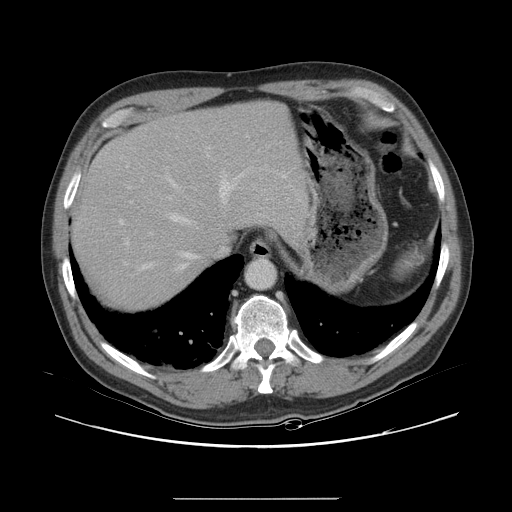
Contrast-enhanced abdominal CT, one axial slice; slice 25 of 40 in the series (ordered by position); 120 kVp; soft-tissue window (W 400 / L 40 HU); 5 mm slice thickness; 512 × 512 image matrix. Male patient, age 64 years. Case-level facts recorded for this patient, not image findings: diagnosis: colorectal cancer liver metastases, imaged before liver resection; multiple liver metastases: yes; largest metastasis: 3.2 cm.
Outlined on this slice (expert manual segmentation):
- hepatic veins: bounding box <125,174,244,271> (left, top, right, bottom; pixels)
- liver: <74,103,306,309>
- planned liver remnant (the part of the liver to remain after resection): <74,103,305,270>
- portal vein (with intrahepatic branches): <119,147,213,244>